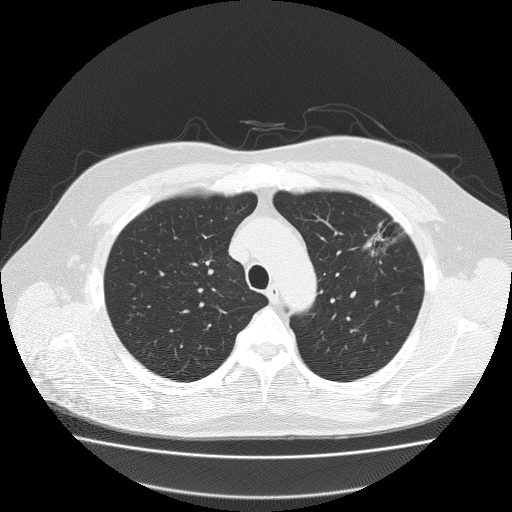
Low-dose screening chest CT, one axial slice; slice 155 of 204 in the series (ordered by position); reconstruction kernel FC51; 120 kVp; lung window (W 1500 / L -600 HU); 2 mm slice thickness; 512 × 512 image matrix, field of view 410 × 410 mm.
Outlined on this slice (manually delineated by an expert):
- lesion 1 (tumor, upper lobe of left lung): bounding box [x1, y1, x2, y2] px = [364, 228, 394, 256]